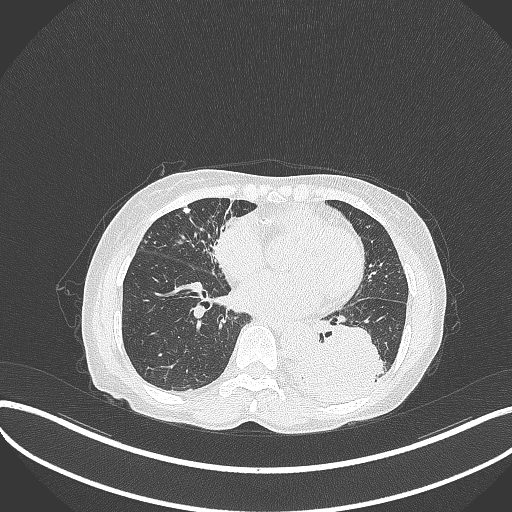
Chest CT, one axial slice. Position 123 of 370 along the scan axis. Reconstruction kernel B70f. Lung window (W 1500 / L -600 HU). 512 × 512 image matrix, field of view 400 × 400 mm. Female patient, age 78 years. From the clinical record (not read from this slice): clinical TNM (as recorded): T3 N0 M1.
Outlined on this slice (bounding box drawn by a radiologist):
- lung tumour (recorded histology: squamous cell carcinoma): bounding box [x1, y1, x2, y2] px = [283, 322, 384, 403]